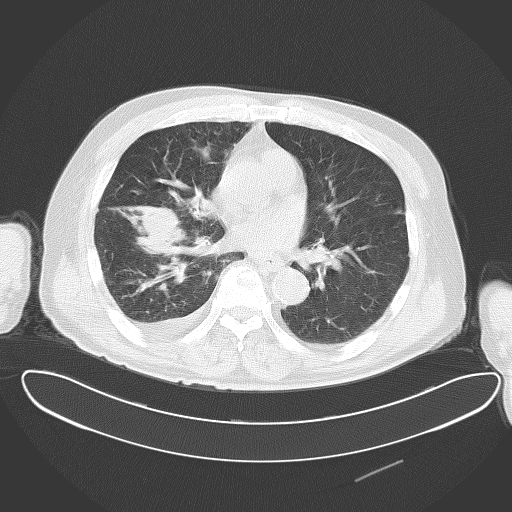
Chest CT, one axial slice. Position 27 of 62 along the scan axis. Reconstruction kernel B70f. 120 kVp. Lung window (W 1500 / L -600 HU). 512 × 512 image matrix, field of view 427 × 427 mm. Male patient, age 78 years. Case-level facts recorded for this patient, not image findings: clinical TNM (as recorded): T2 N1 M1.
Structures marked on this image (bounding box drawn by a radiologist):
- lung tumour (recorded histology: adenocarcinoma): bounding box [x1, y1, x2, y2] px = [128, 199, 194, 269]